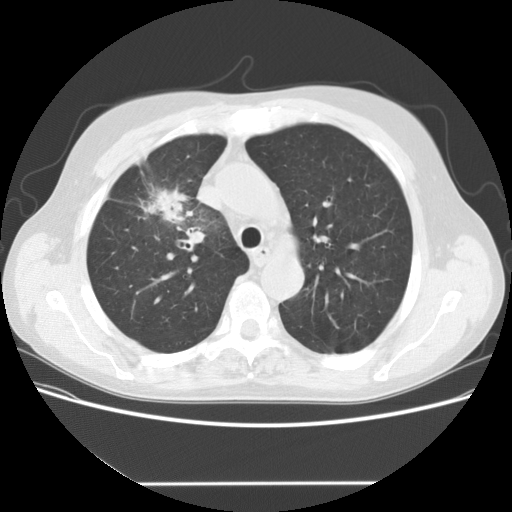
Axial slice from a low-dose chest CT screening exam; first (baseline) screen; lung window (W 1500 / L -600 HU); 2.5 mm slice thickness; 120 kVp; slice 43 of 153 in the series; 512 × 512 image matrix, field of view 360 × 360 mm. Male, age 56 years at enrolment. Current smoker at enrolment.
Expert reader's lesion annotation, bounding box <127,170,217,249> (left, top, right, bottom; pixels). The screening reader recorded 2 non-calcified nodules or masses ≥4 mm on this exam (right upper lobe, right middle lobe); which of them this box marks is not recorded. Later outcome: lung cancer diagnosed 120 days after this screen — adenocarcinoma, NOS, right upper lobe, stage IIIA (AJCC 6th edition), 34 mm at pathology.